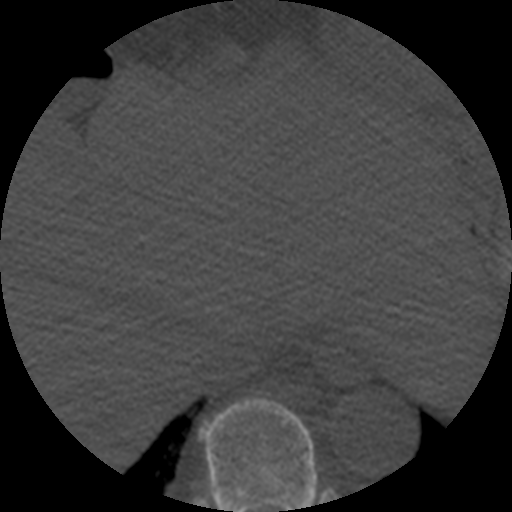
CT including the spine, one axial slice; slice 293 of 508 in the series (ordered by position); bone window (W 1800 / L 400 HU); 512 × 512 image matrix, field of view 160 × 160 mm. Patient age 57 years. From the clinical record (not read from this slice): primary cancer: prostate.
Outlined on this slice (semi-automatically segmented with operator editing):
- T9 vertebra: box from (x=200, y=397) to (x=317, y=512) px